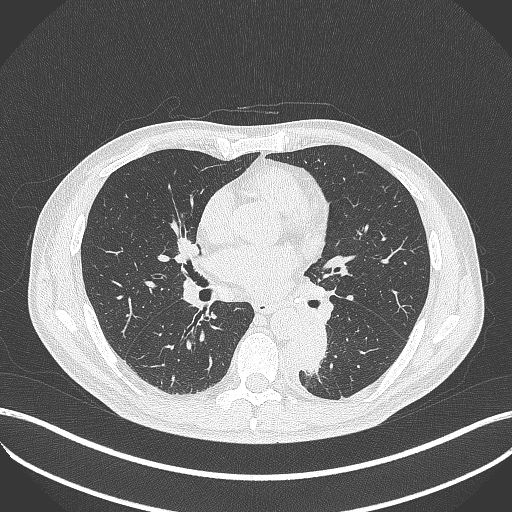
Chest CT, one axial slice; position 206 of 451 along the scan axis; reconstruction kernel B70f; lung window (W 1500 / L -600 HU); 1 mm slice thickness; 512 × 512 image matrix. Male patient, age 72 years. From the clinical record (not read from this slice): clinical TNM (as recorded): T2b N0 M1.
Outlined on this slice (bounding box drawn by a radiologist):
- lung tumour (recorded histology: adenocarcinoma): bounding box (x1, y1, x2, y2) in pixels: (282, 314, 331, 386)